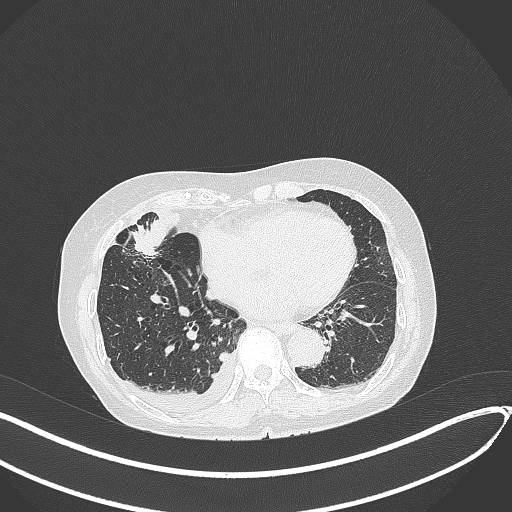
Chest CT, one axial slice. Position 138 of 418 along the scan axis. Lung window (W 1500 / L -600 HU). 1 mm slice thickness. 512 × 512 image matrix. Patient: female, 75 years. From the clinical record (not read from this slice): clinical TNM (as recorded): T2a N3 M0.
Structures marked on this image (rectangle marked by the reading radiologist):
- lung tumour (recorded histology: adenocarcinoma): box from (x=133, y=228) to (x=159, y=257) px